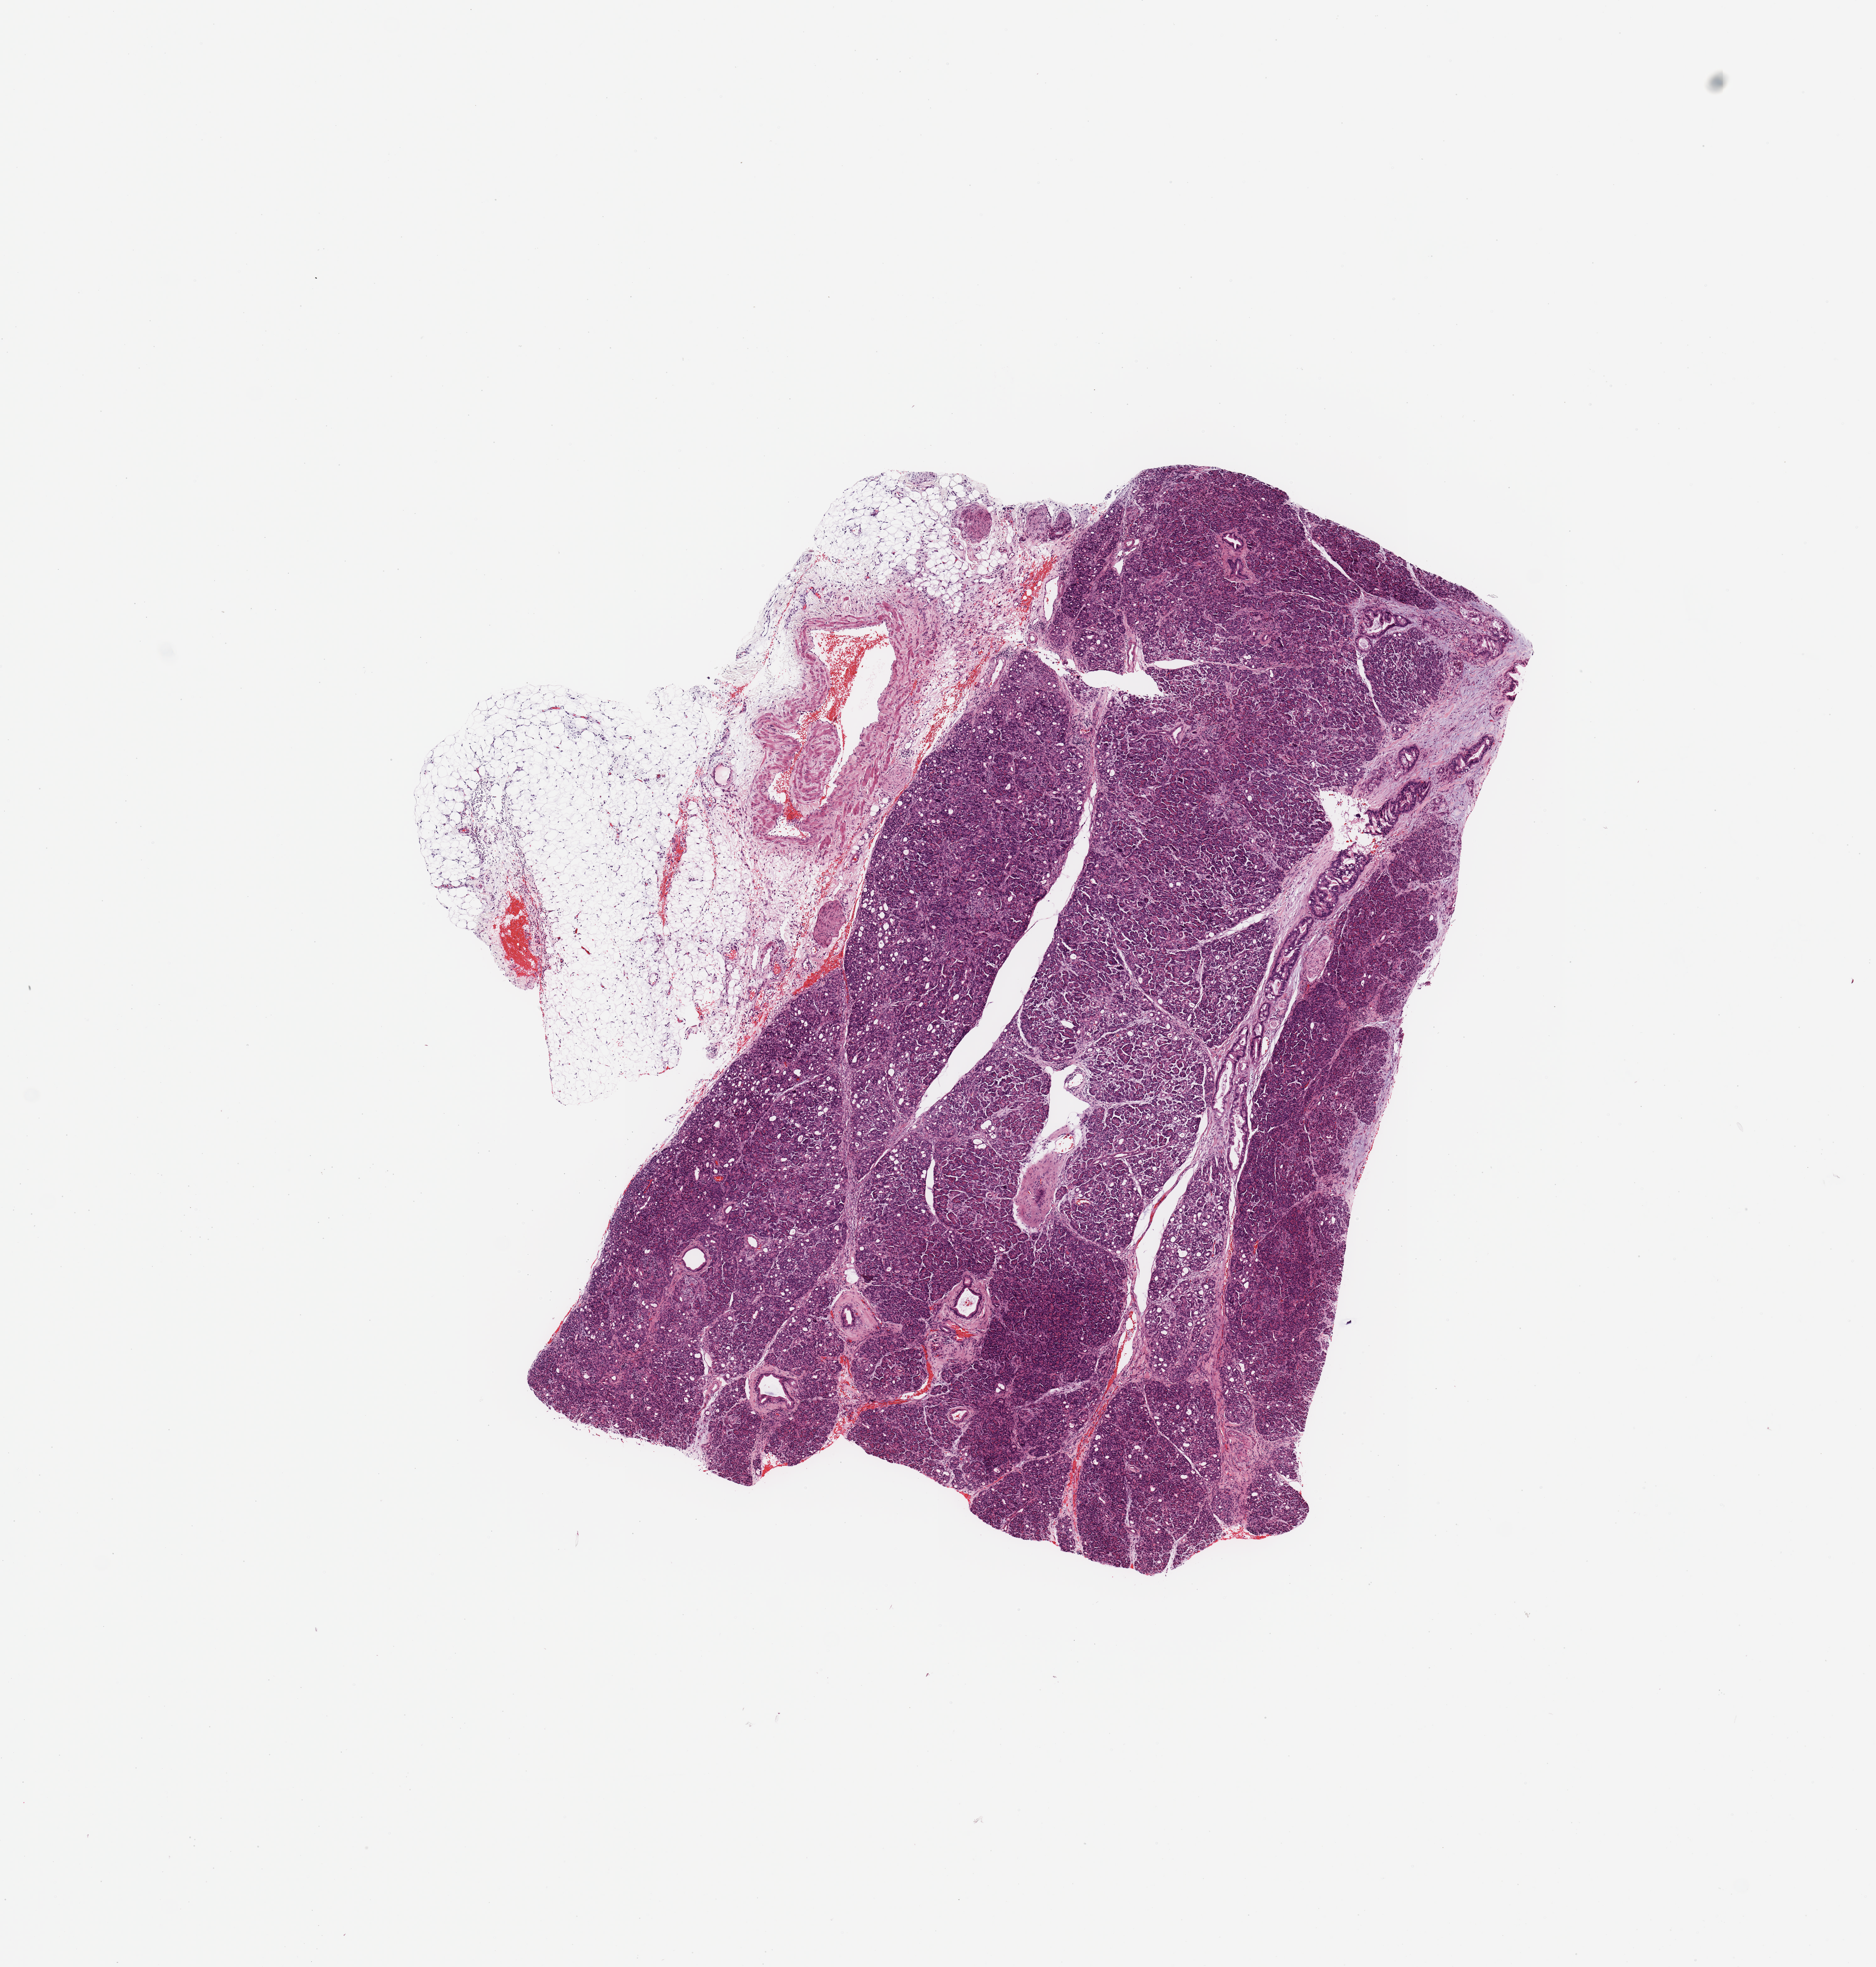
H&E whole-slide image — low-resolution overview of the scanned area, about 11.8 x 12.4 mm (acquisition: 20x scan); tumour tissue sample, pancreas. Patient: female, age 60 years. Histologic grade: G2 (moderately differentiated).
- primary tumour site (as recorded): head
- diagnosis: Infiltrating duct carcinoma, NOS
- AJCC pathologic stage: IIB